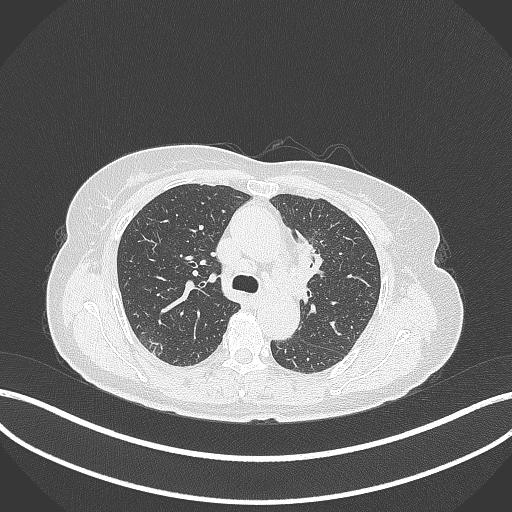
Chest CT, one axial slice. Position 226 of 369 along the scan axis. Reconstruction kernel B70f. Lung window (W 1500 / L -600 HU). 512 × 512 image matrix, field of view 400 × 400 mm. Patient: female, 65 years. Case-level facts recorded for this patient, not image findings: clinical TNM (as recorded): T2a N0 M0.
Structures marked on this image (rectangle marked by the reading radiologist):
- lung tumour (recorded histology: adenocarcinoma): bounding box (x1, y1, x2, y2) in pixels: (293, 230, 327, 286)